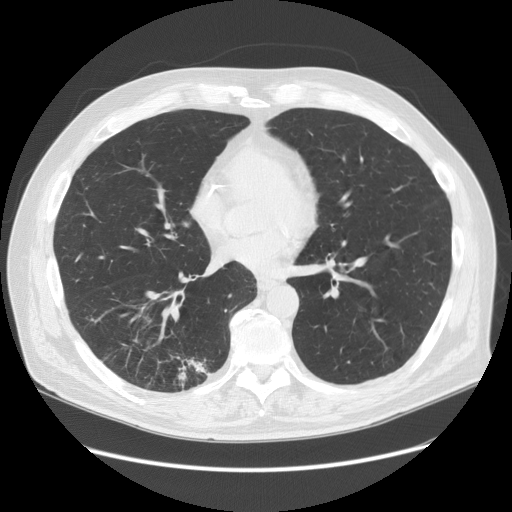
Low-dose screening chest CT, one axial slice. Slice 65 of 149 in the series (ordered by position). 120 kVp. Lung window (W 1500 / L -600 HU). 2.5 mm slice thickness. 512 × 512 image matrix.
Structures marked on this image (expert manual segmentation):
- lesion 1 (tumor, lower lobe of right lung): box from (x=178, y=359) to (x=207, y=381) px